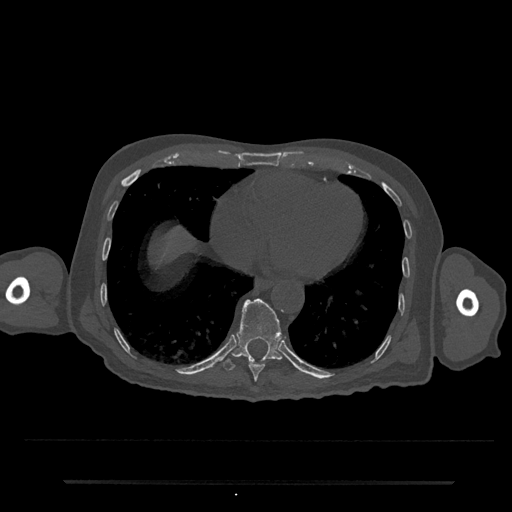
CT including the spine, one axial slice. Position 335 of 797 along the scan axis. Reconstruction kernel Br40s/3. 120 kVp. Bone window (W 1800 / L 400 HU). 0.5 mm slice thickness. 512 × 512 image matrix, field of view 427 × 427 mm. Male patient, age 74 years. Case-level facts recorded for this patient, not image findings: primary cancer: prostate.
Annotated regions visible in this slice (semi-automatically segmented with operator editing):
- T10 vertebra: box from (x=223, y=298) to (x=283, y=371) px
- T9 vertebra: (x=249, y=361)–(x=265, y=382)